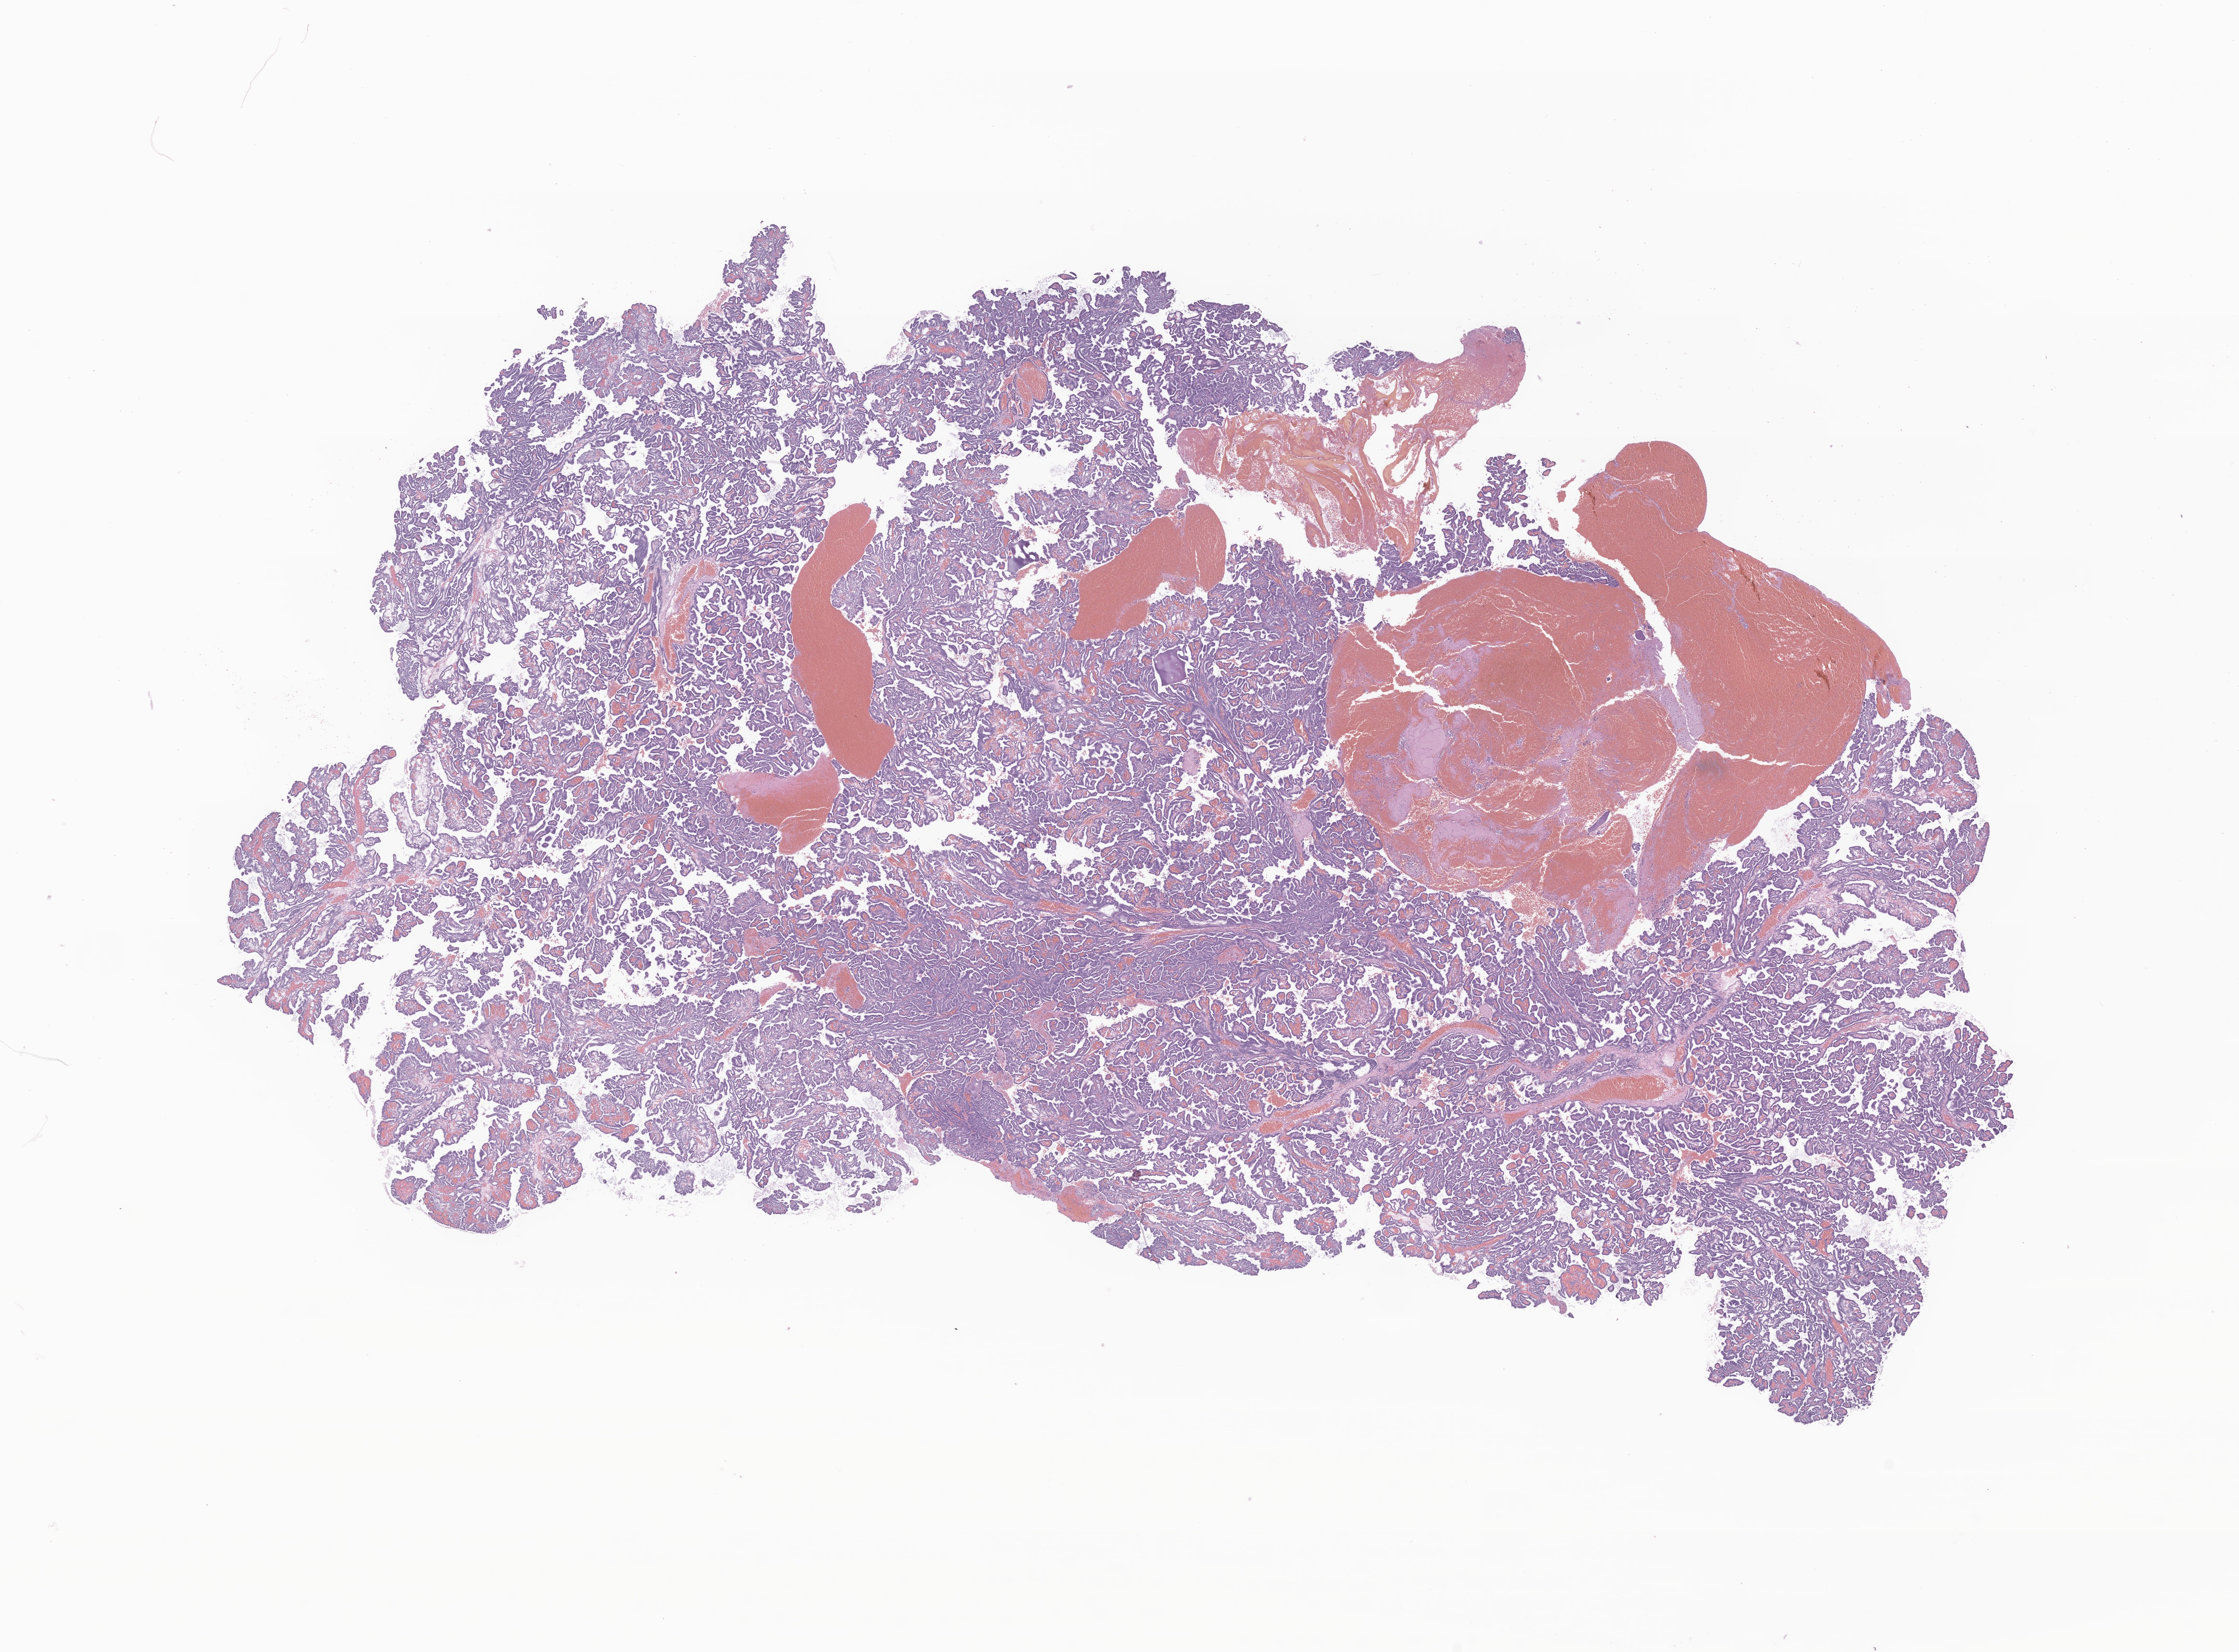
Digitized haematoxylin and eosin-stained section of tumor tissue from the brain, whole scanned area (about 19.6 x 14.5 mm) shown as a low-resolution overview, formalin-fixed, paraffin-embedded (FFPE) tissue. Patient female; age 156 days.
Diagnosis (ICD-O-3 morphology term): Carcinoma, NOS.